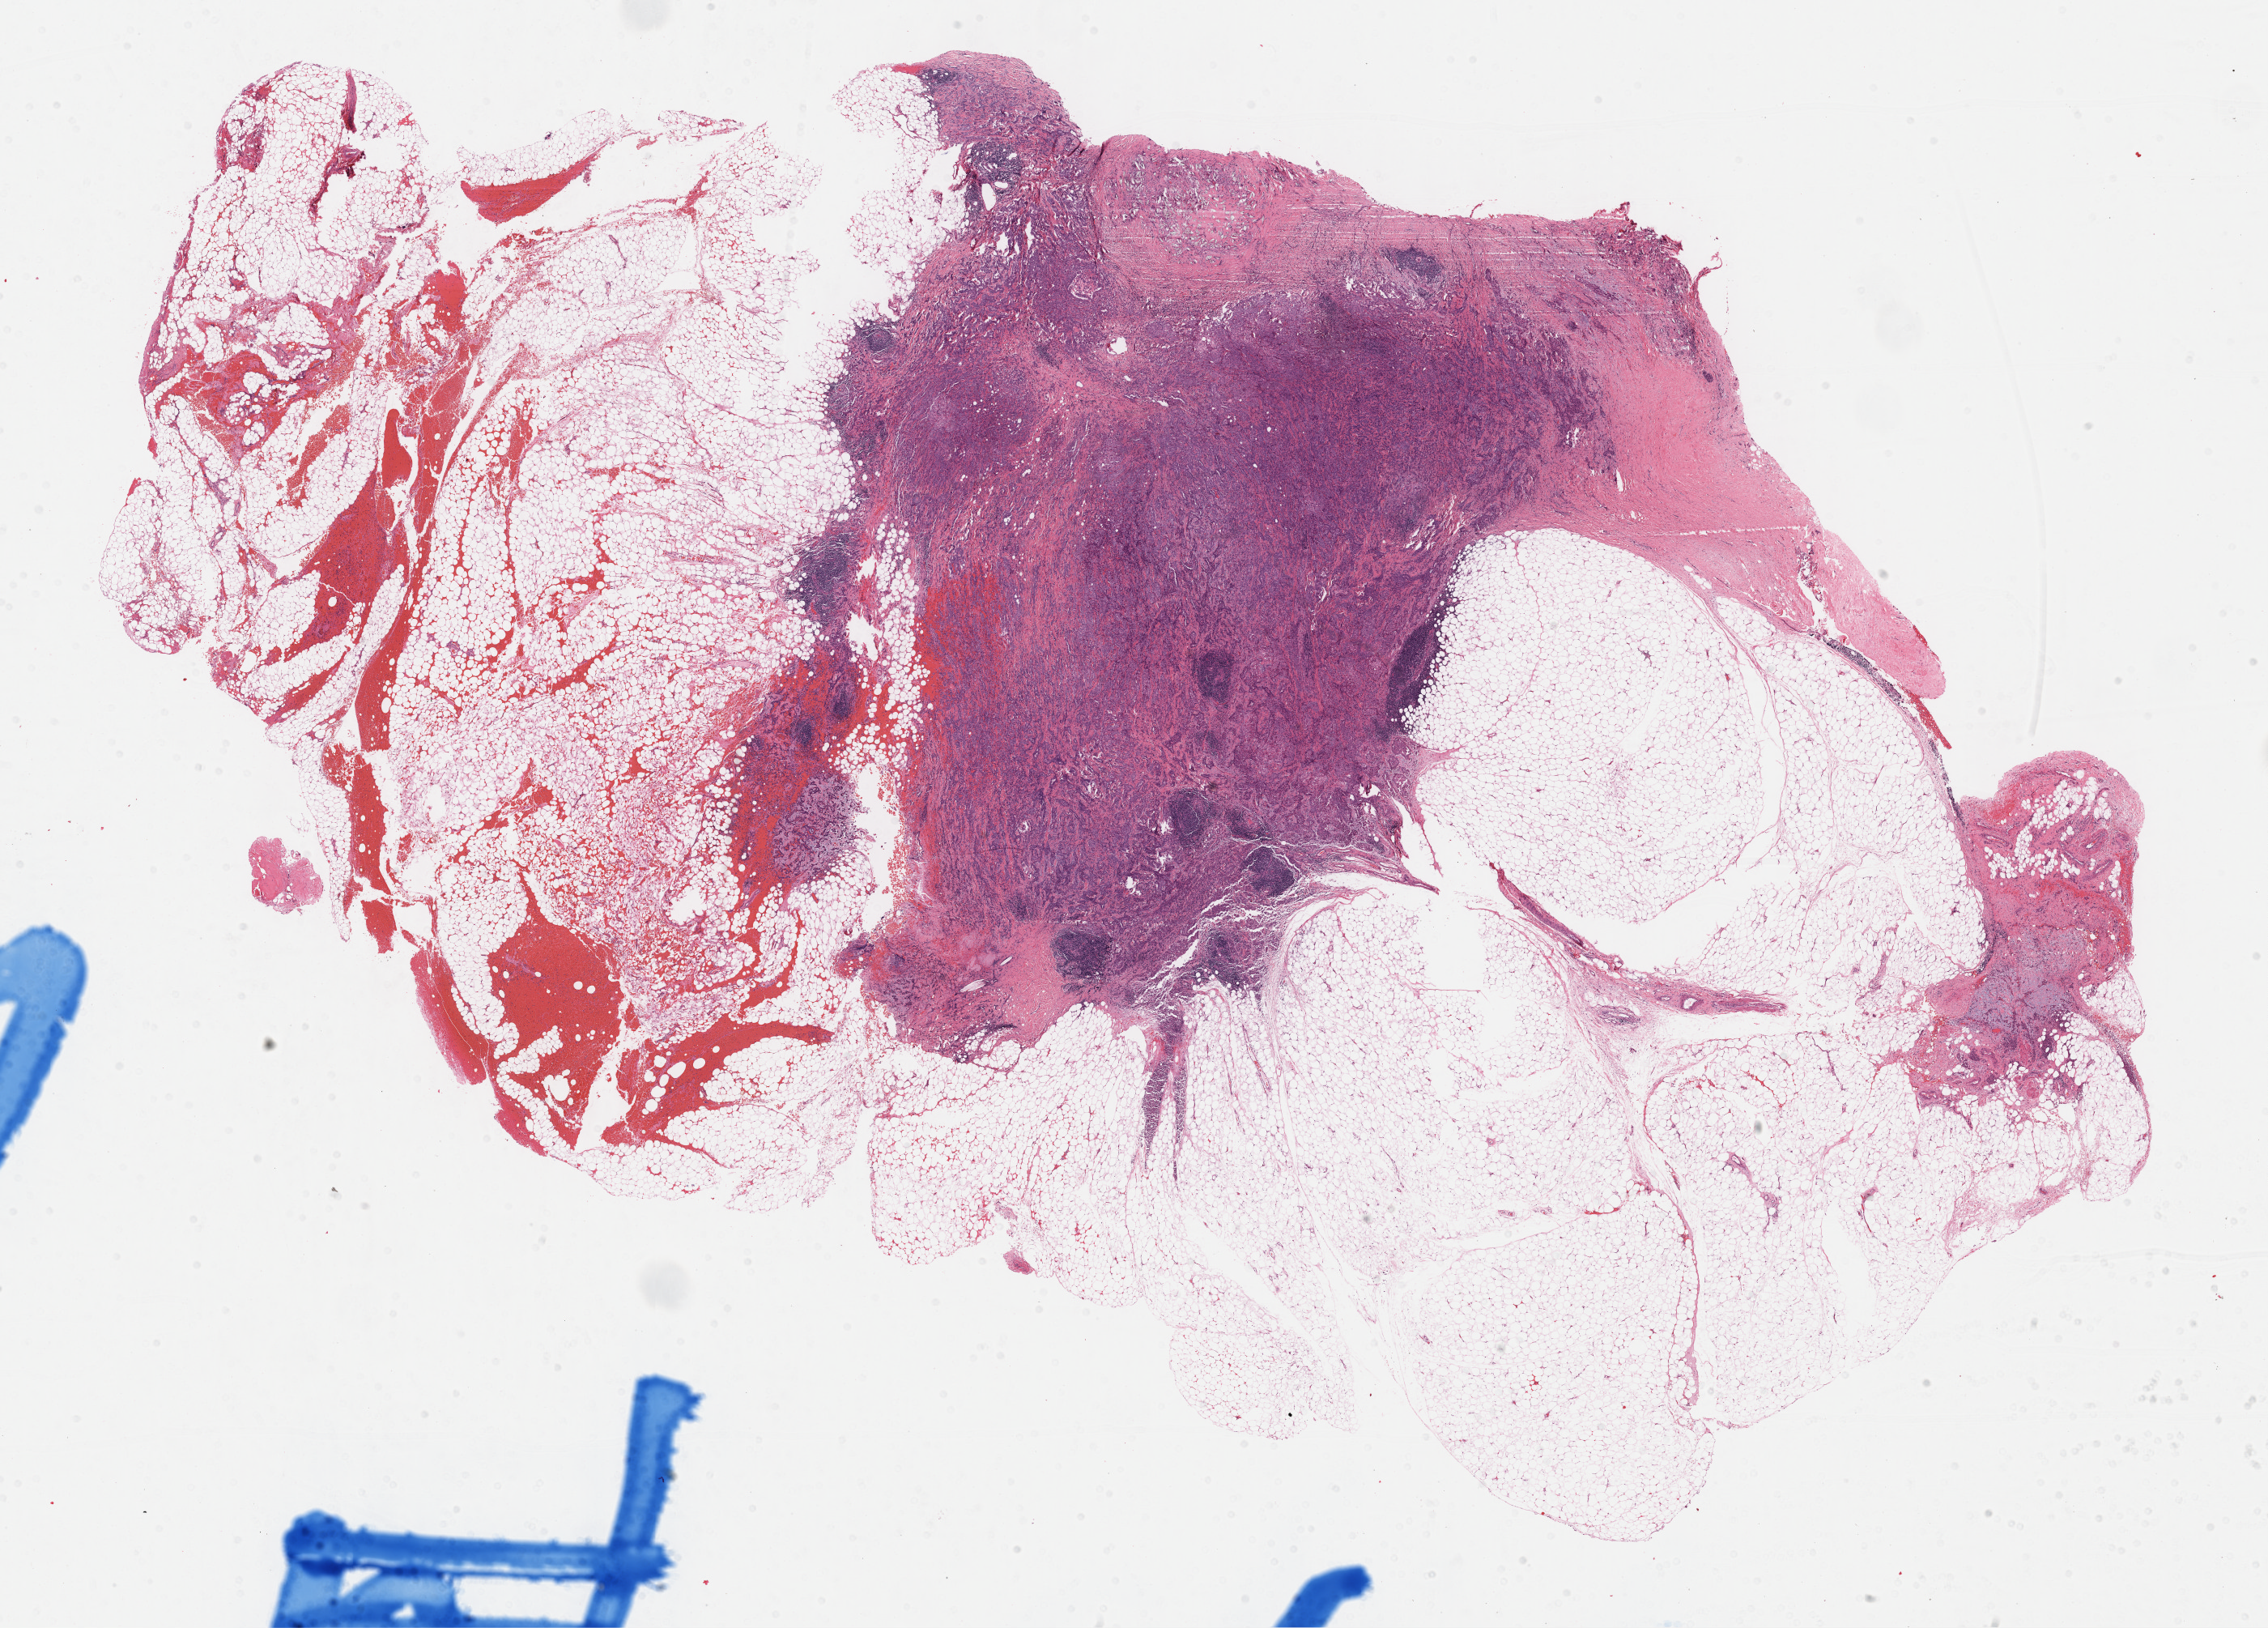
Digitized H&E-stained tissue section (whole slide), a low-resolution overview of the entire scanned area, about 22.7 x 16.3 mm (from a 40x scan). FFPE section. Mesothelium, primary tumour sample. Male, age 62 years at initial diagnosis.
• AJCC pathologic stage: III
• pathologic diagnosis: Mesothelioma, biphasic, malignant (pleura, NOS)
• laterality: left